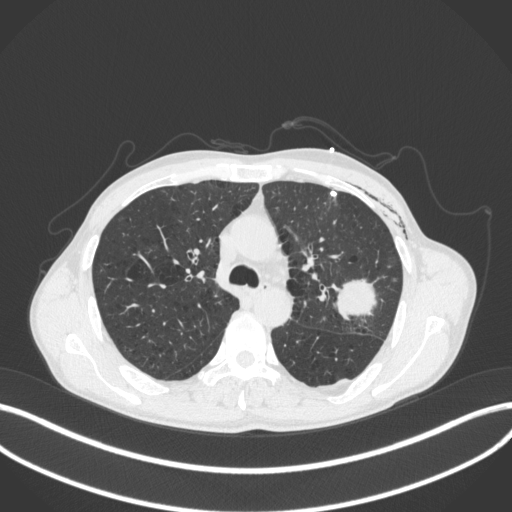
Chest CT, one axial slice. Slice 271 of 416 in the series (ordered by position). Reconstruction kernel B31f. 120 kVp. Lung window (W 1500 / L -600 HU). 1 mm slice thickness. 512 × 512 image matrix, field of view 400 × 400 mm. Patient: male, 58 years. From the clinical record (not read from this slice): clinical TNM (as recorded): T3 N0 M0.
Outlined on this slice (rectangle marked by the reading radiologist):
- lung tumour (recorded histology: adenocarcinoma): bounding box [x1, y1, x2, y2] px = [332, 272, 388, 324]